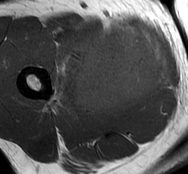
MRI of an extremity soft-tissue mass, one axial slice; slice 34 of 93 in the series (ordered by position); MR volume resampled by the dataset authors to the PET/CT grid (not the native acquisition matrix); 3.27 mm slice thickness; 188 × 174 image matrix. Male patient. Case-level facts recorded for this patient, not image findings: histological type: undifferentiated - pleiomorphic; grade: high; site of the primary tumour: right thigh.
Structures marked on this image (expert contour drawn on MRI and transferred to this co-registered scan by the dataset authors):
- gross tumour volume including surrounding oedema: bounding box (x1, y1, x2, y2) in pixels: (49, 24, 169, 114)
- gross tumour volume (mass): (72, 24, 169, 114)